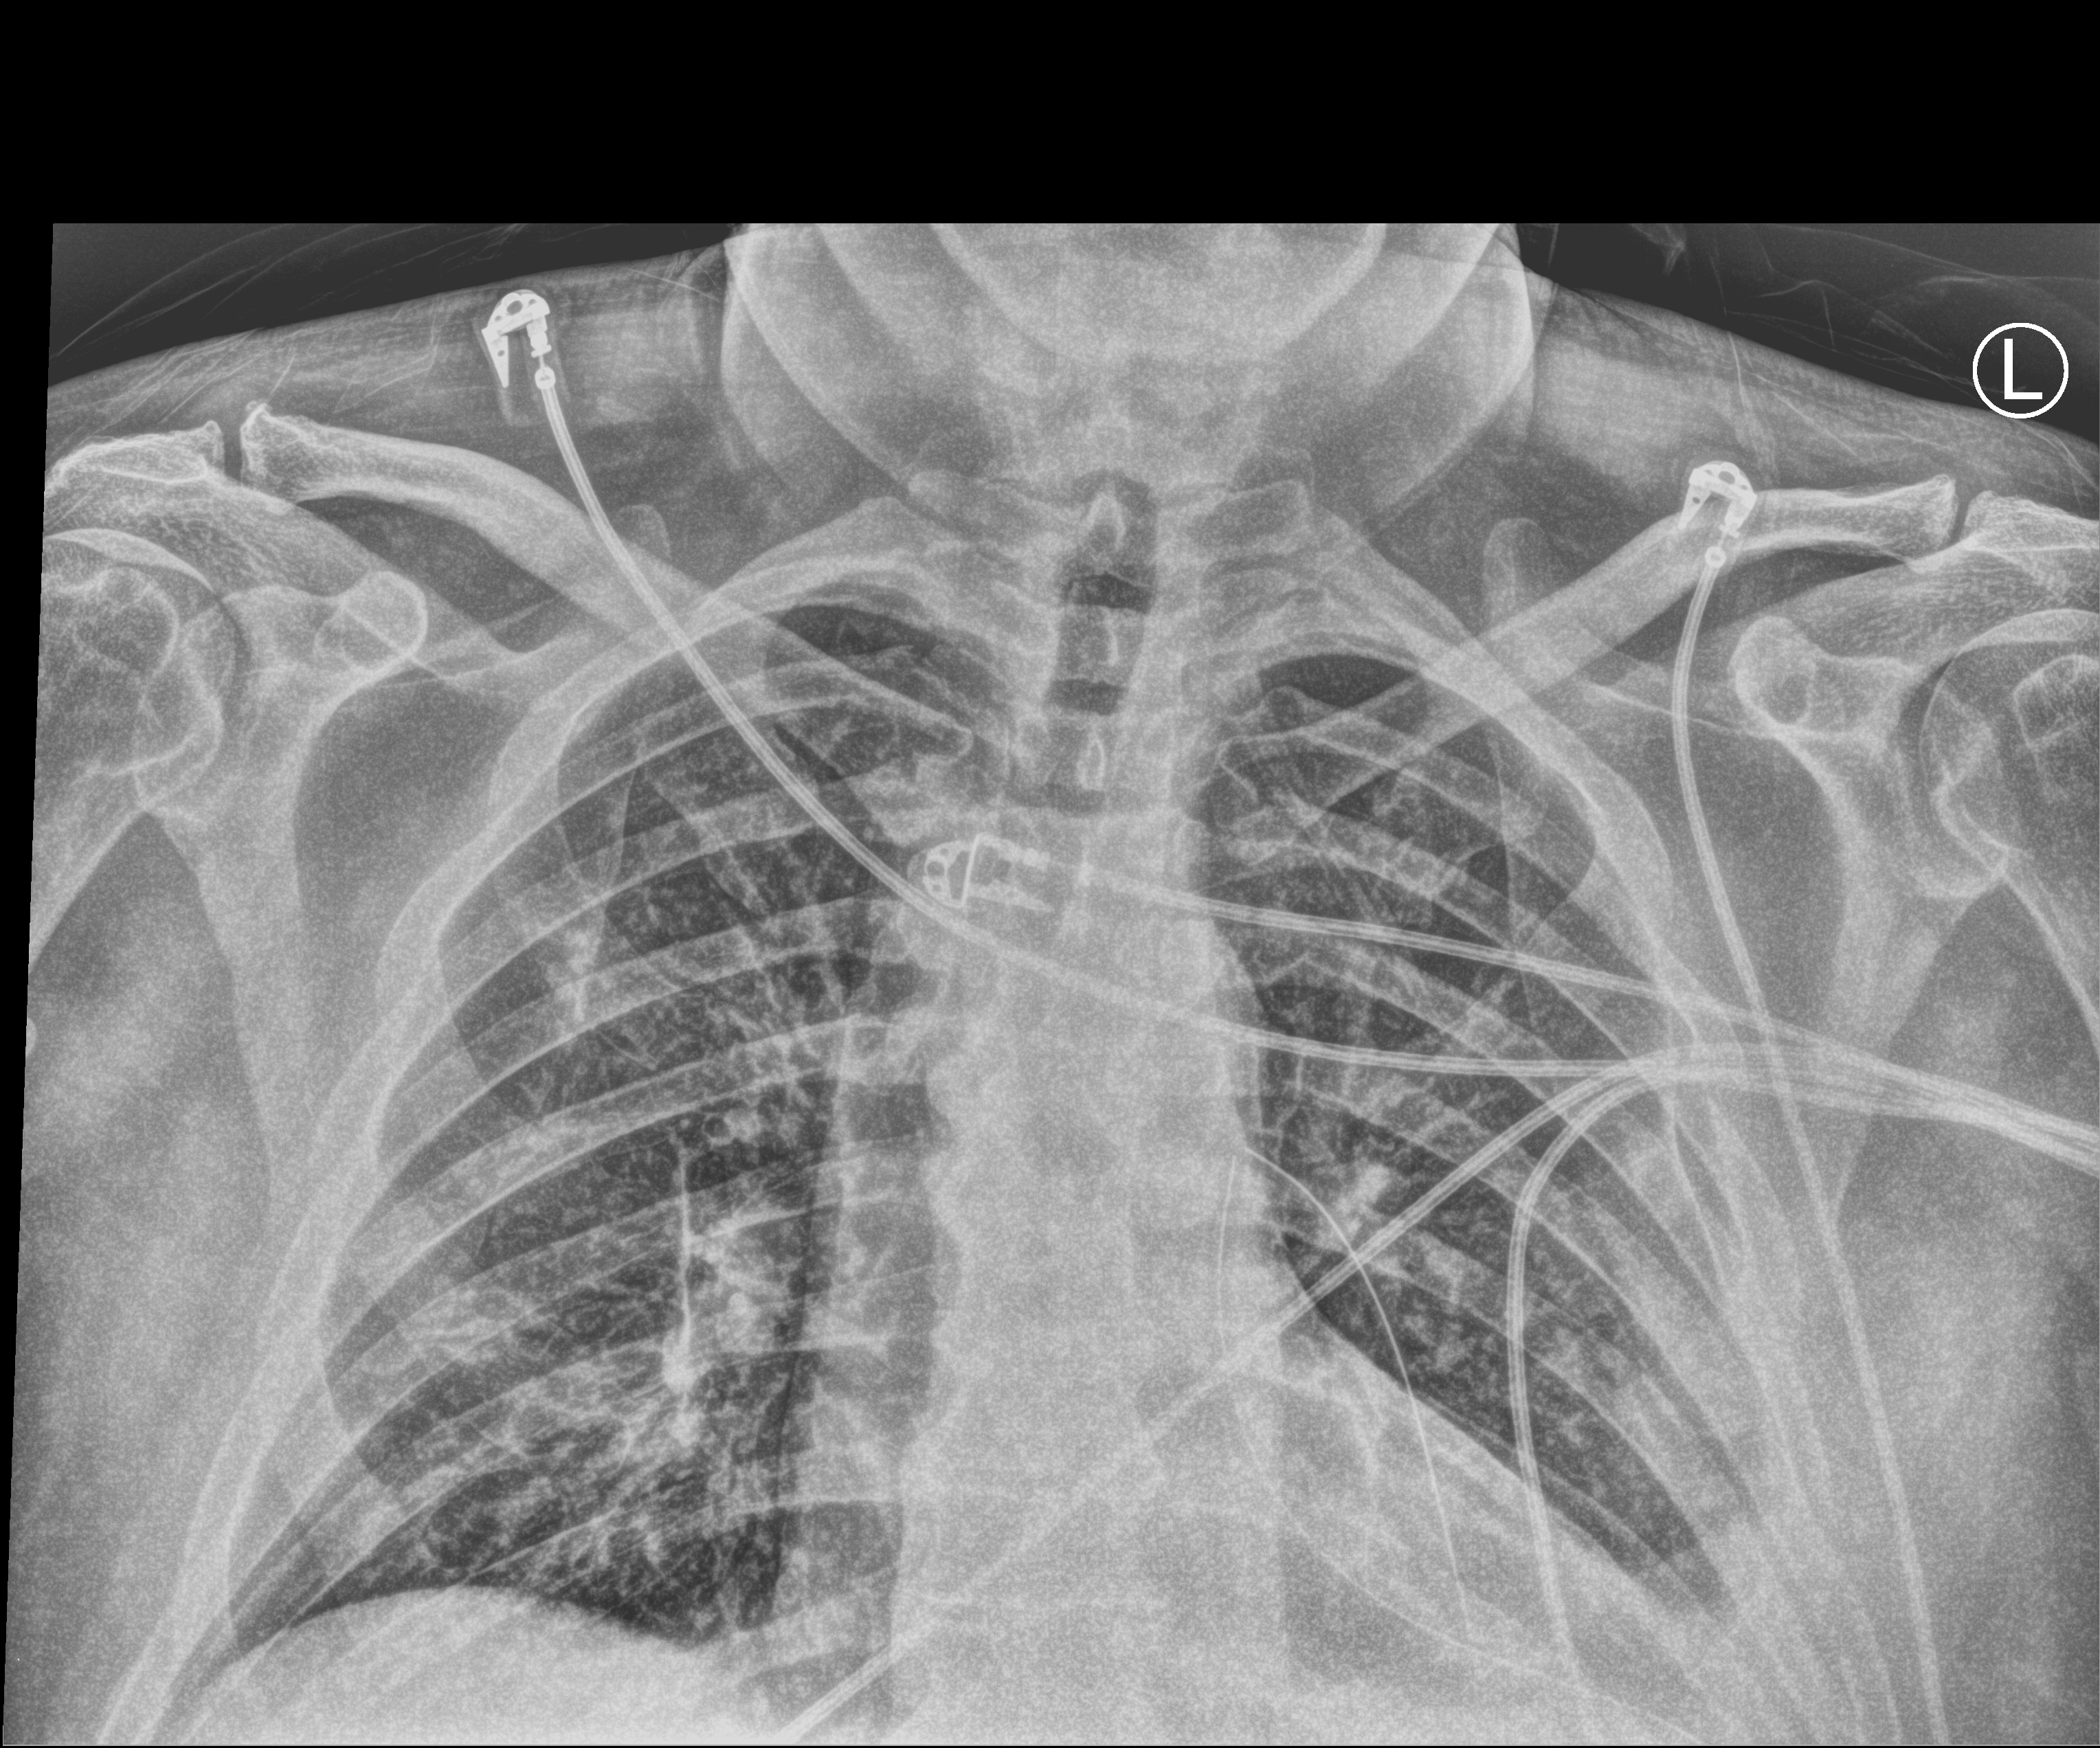
Chest X-ray (portable), anteroposterior (AP) projection. Male patient hospitalised with COVID-19, age 18–59 years.
Admission-level facts for this patient (not findings on this image; timing relative to this image not recorded): mechanically ventilated during this hospital stay: no.